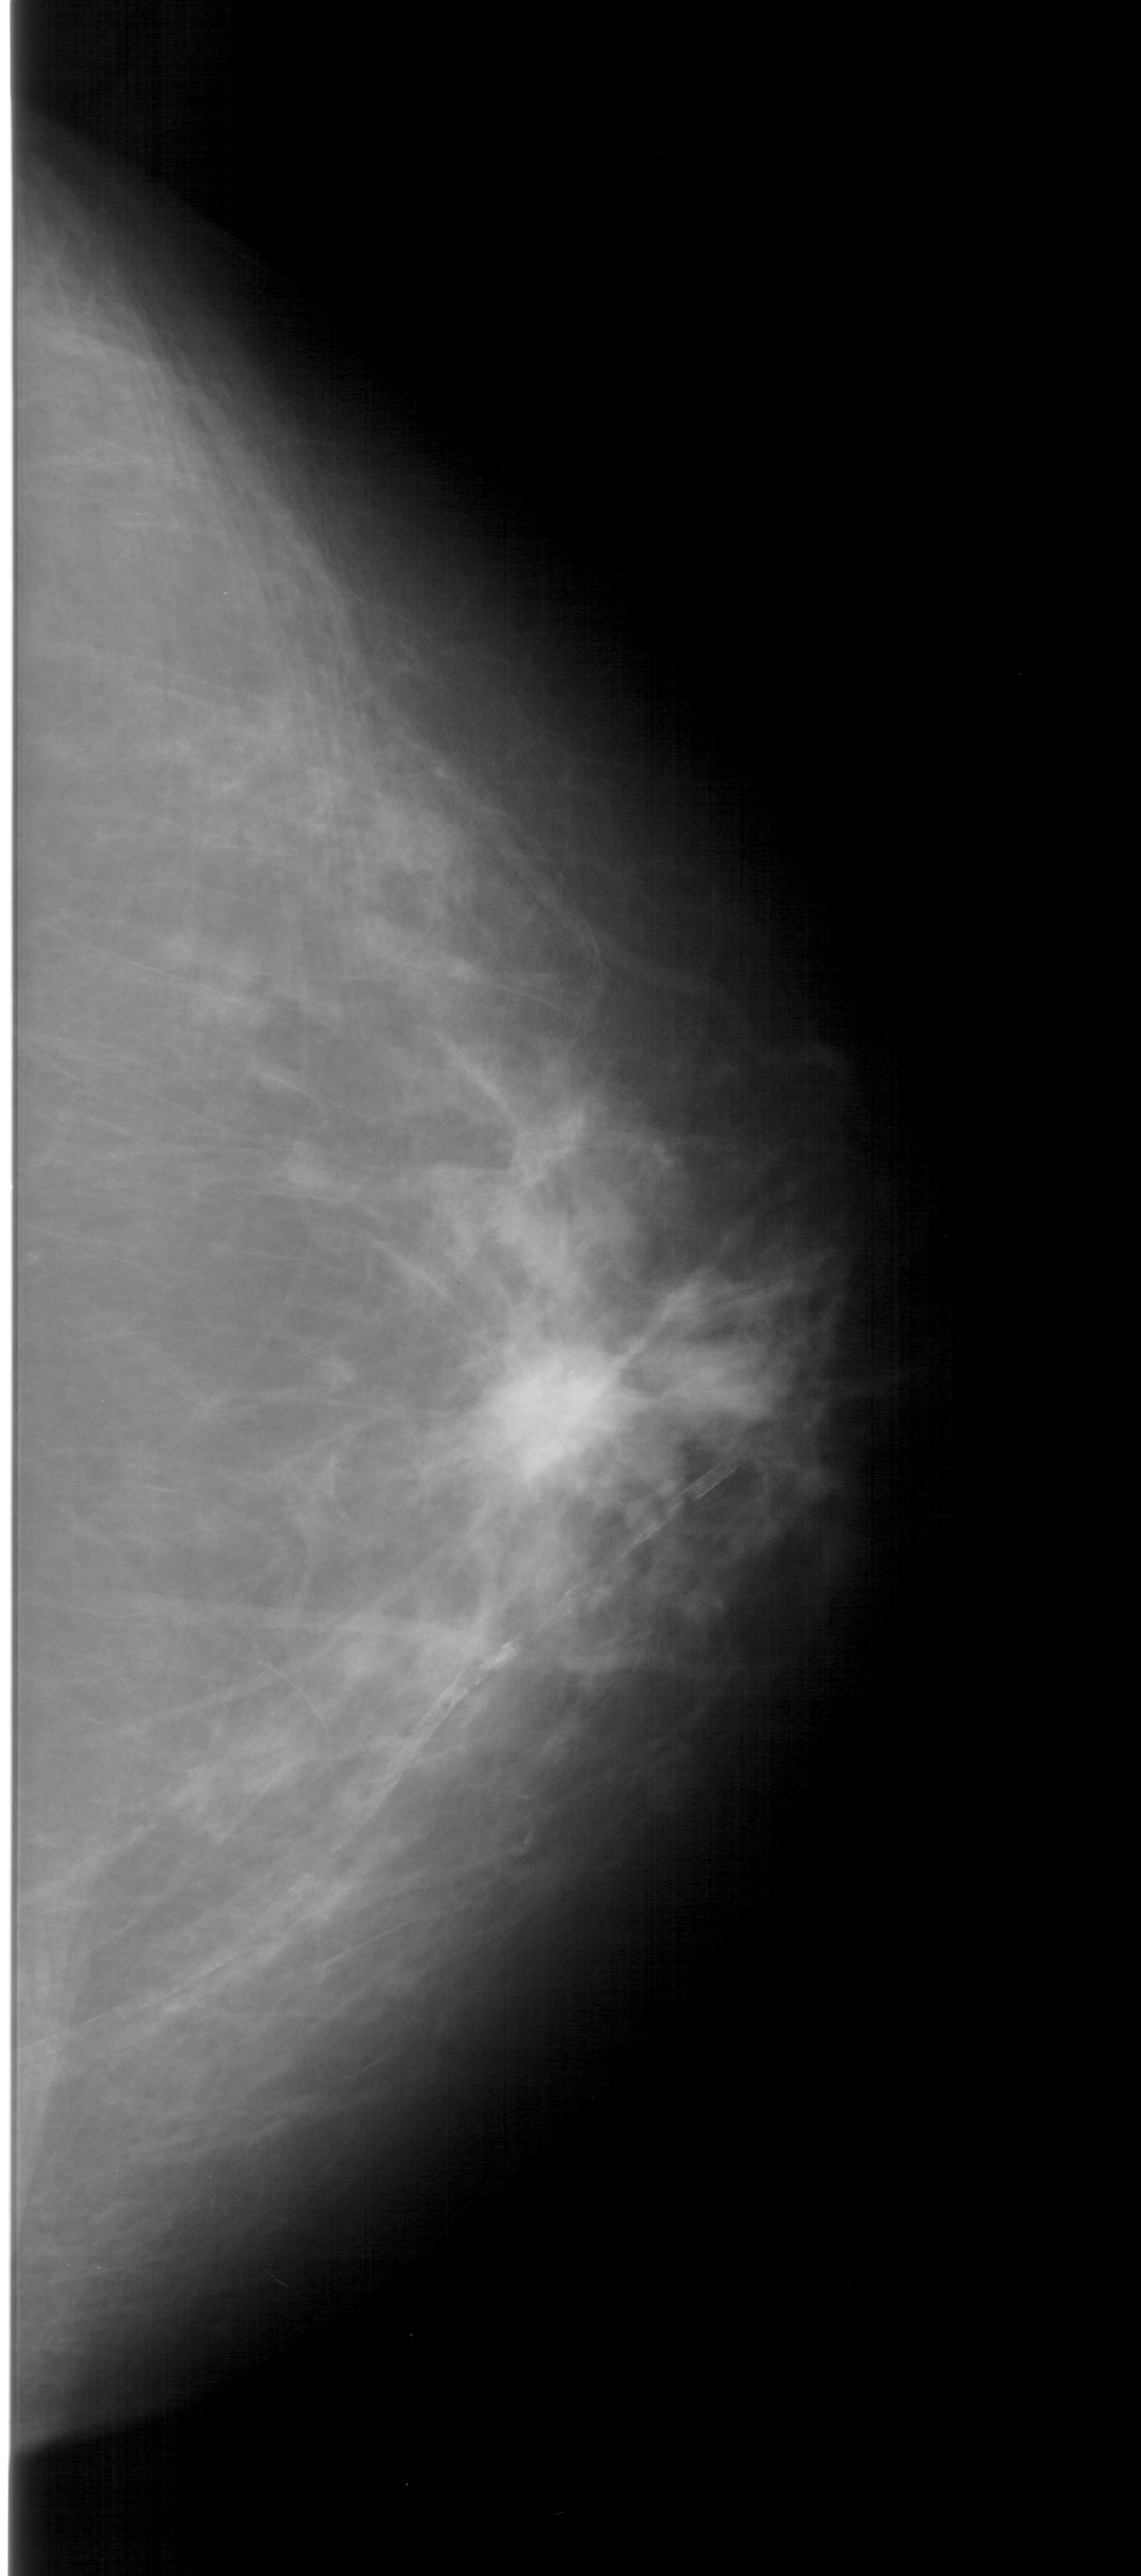
Digitized screen-film mammogram; right breast; CC view; breast composition: heterogeneously dense (BI-RADS density category 3 of 4).
- Finding: calcifications, morphology pleomorphic, distribution clustered; BI-RADS assessment category 5; pathology result (as recorded, not read from the image): malignant.